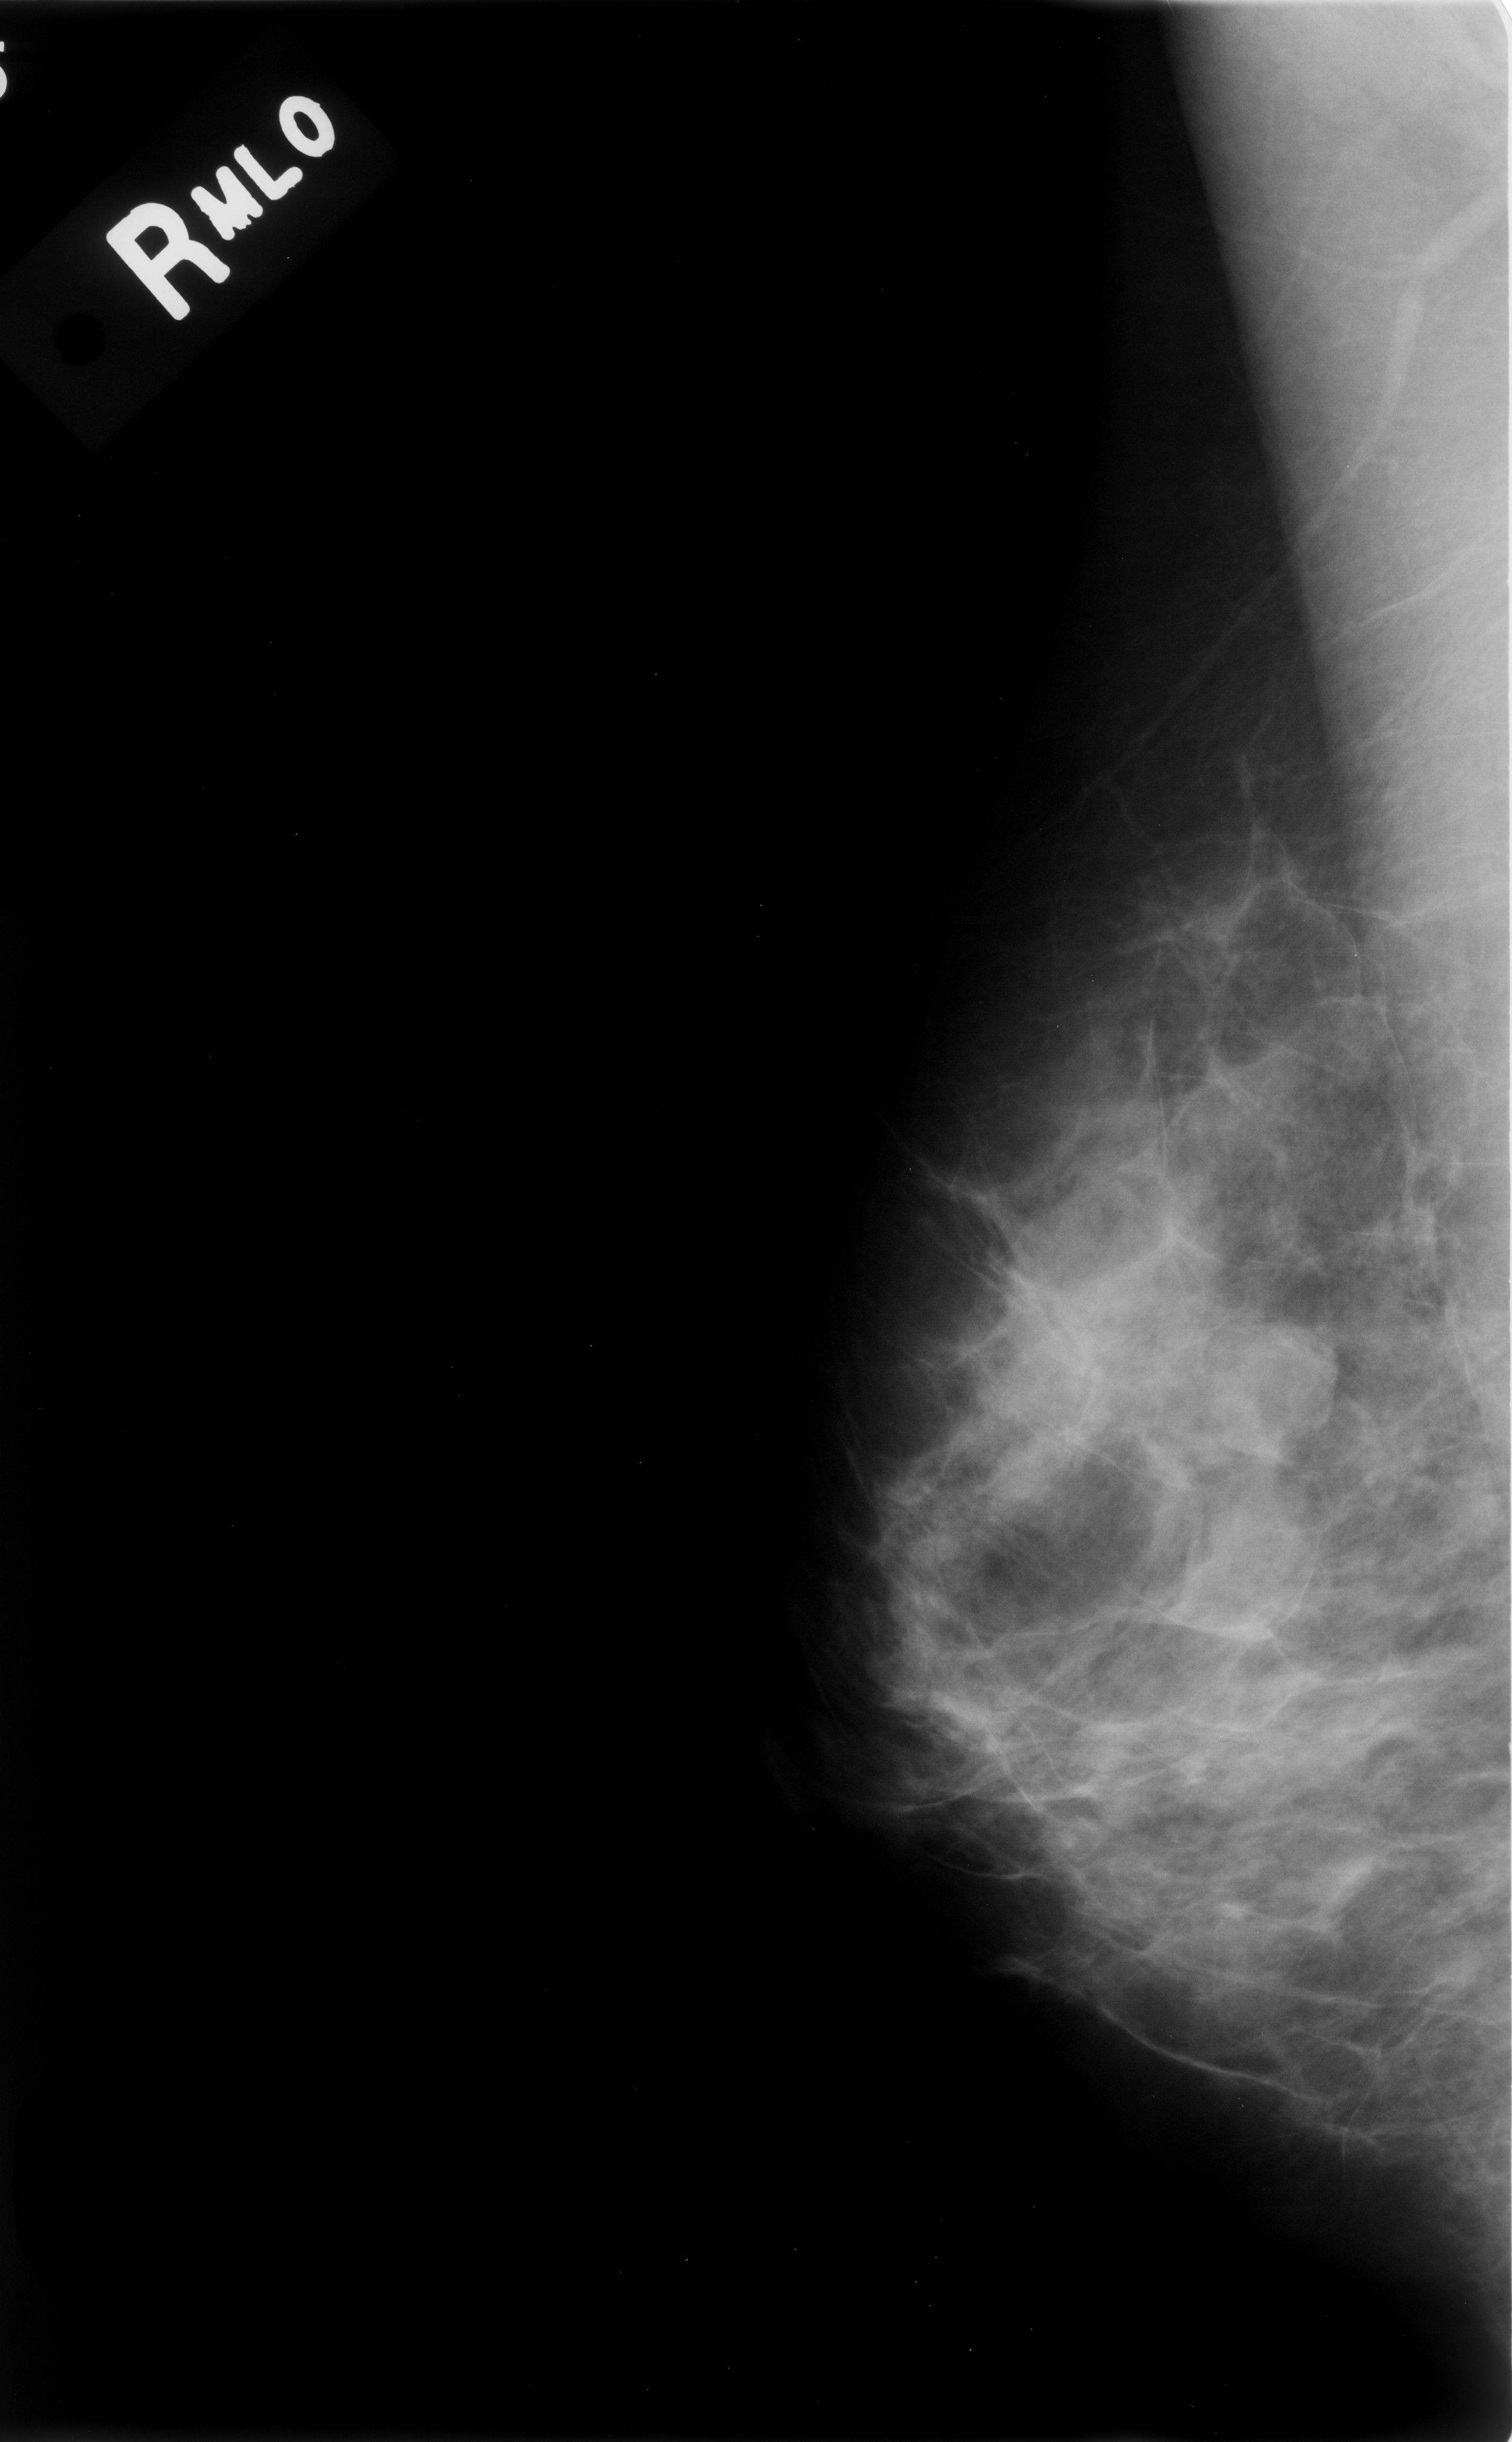
Mammogram (digitized film), right breast, mediolateral oblique (MLO) view, BI-RADS breast density category 2 (scale 1–4).
- Abnormality record for this image: mass, shape round, margins circumscribed; BI-RADS assessment category 3; subtlety rating 3 on a 1 (subtle) to 5 (obvious) scale; pathology (as recorded): benign.